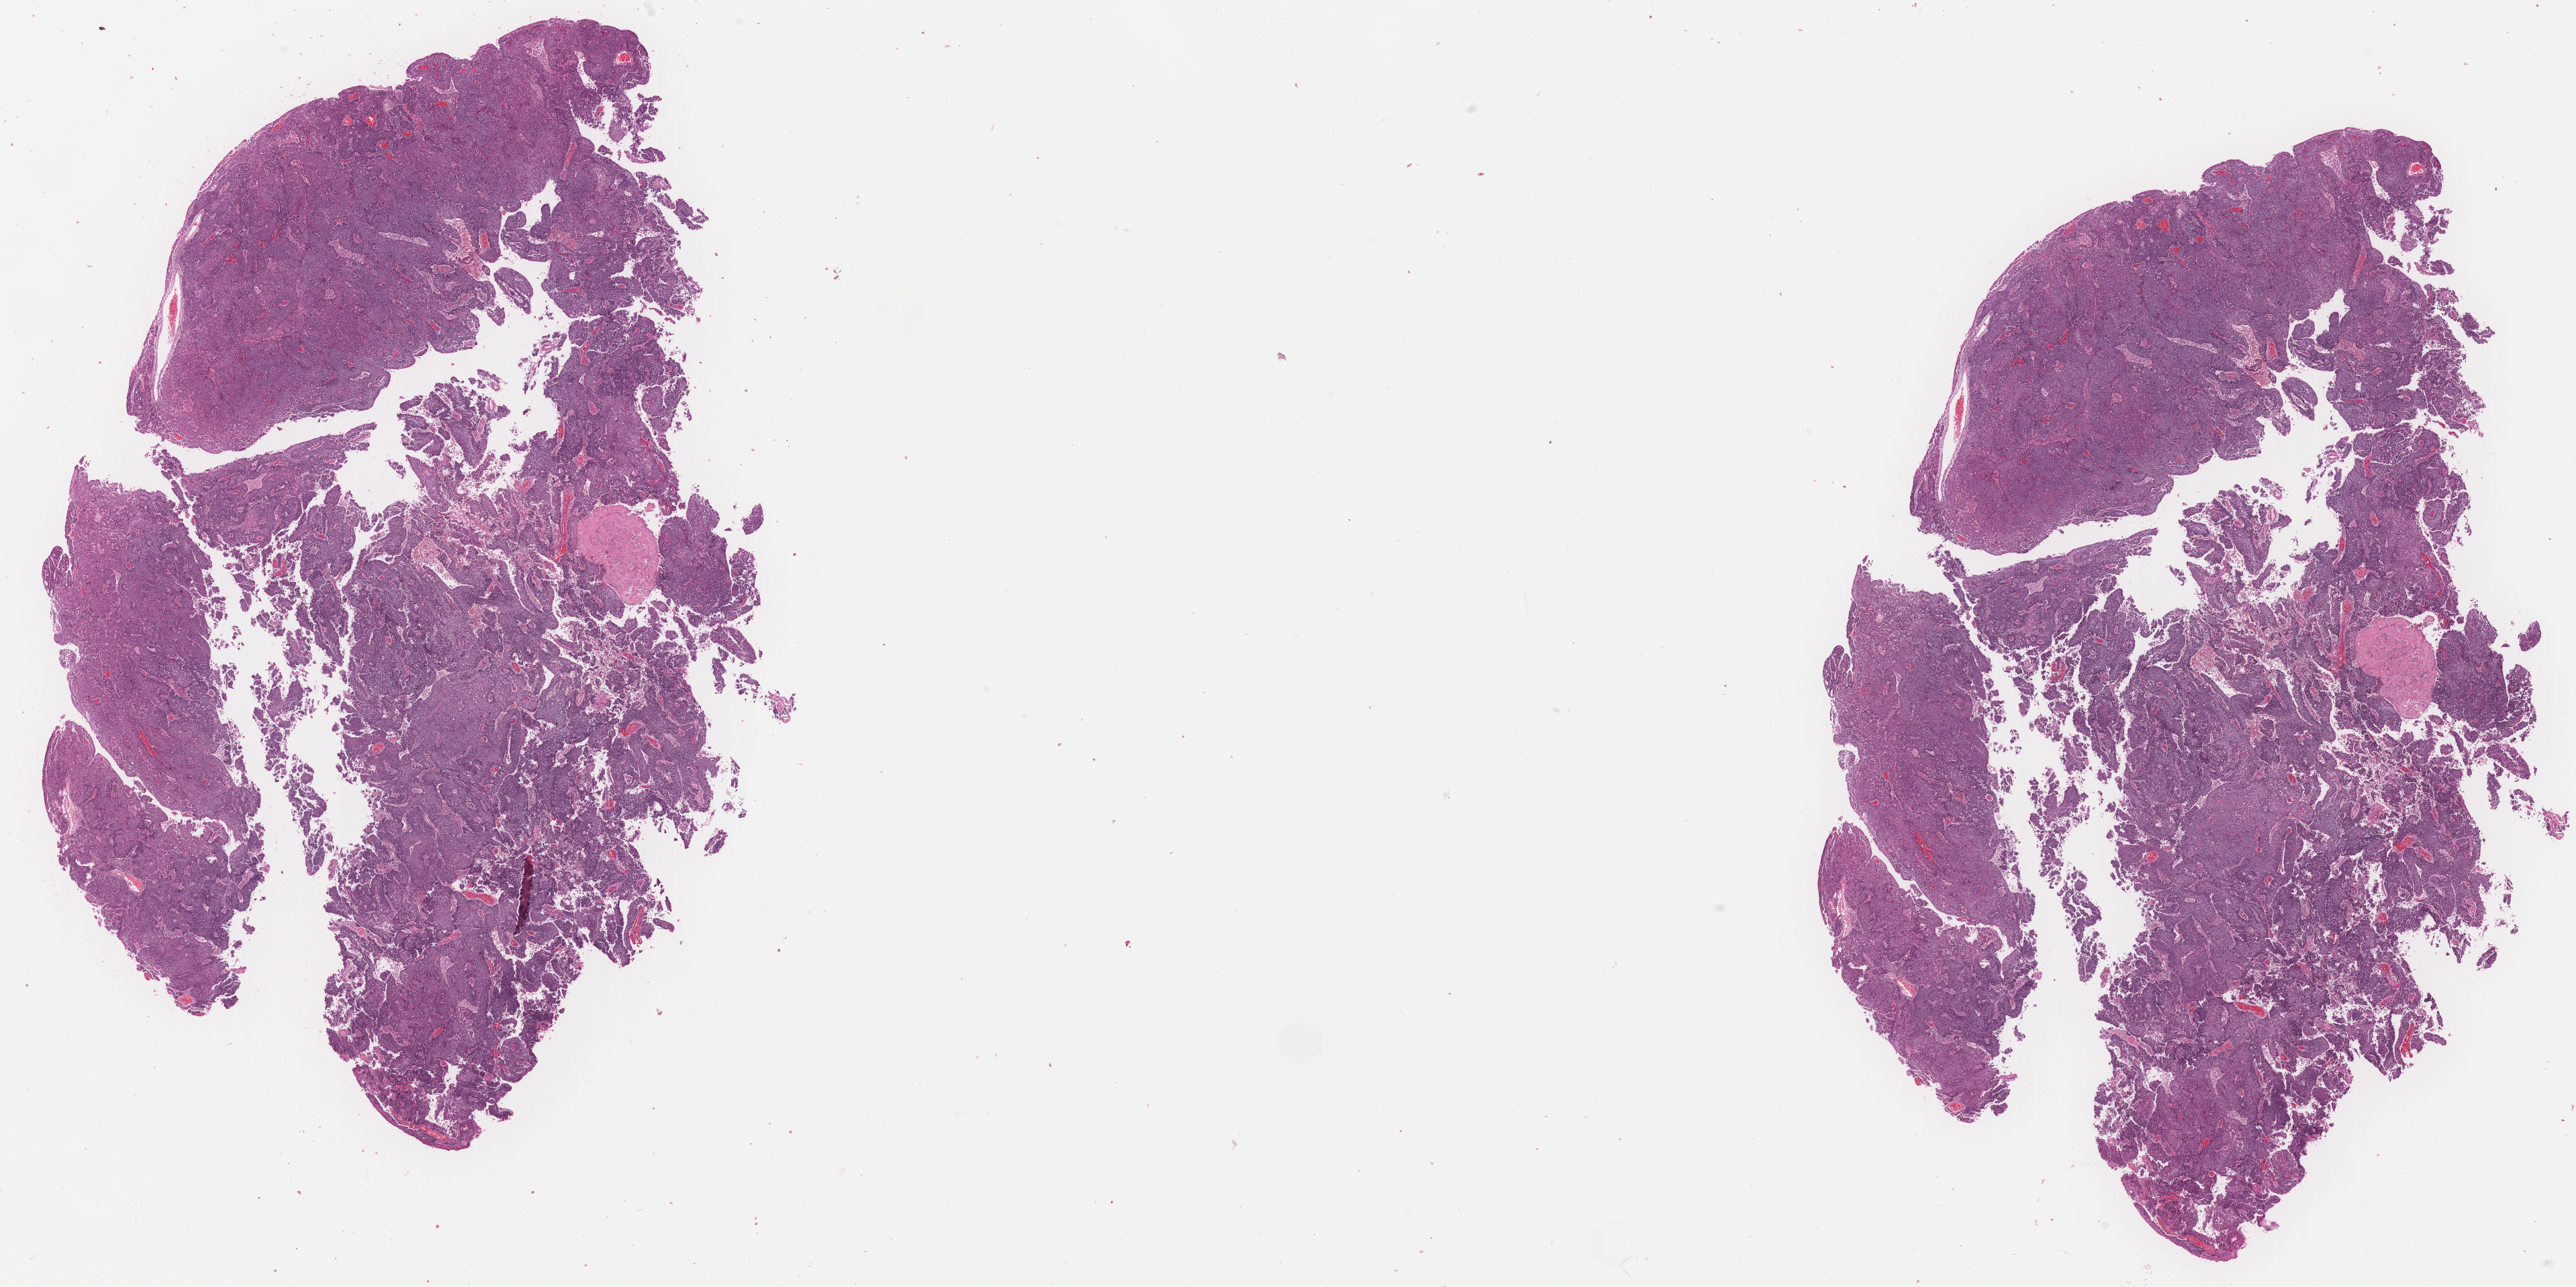
Hematoxylin and eosin (H&E) stained whole-slide image, low-resolution overview of the scanned area, about 30.4 x 15.2 mm (slide scanned at 40x). FFPE section. Sample: primary tumour, uterus. Female, age 60 years at initial diagnosis. Histologic grade: G3 (poorly differentiated).
FIGO stage: IB. Pathologic diagnosis: Endometrioid adenocarcinoma, NOS (endometrium).